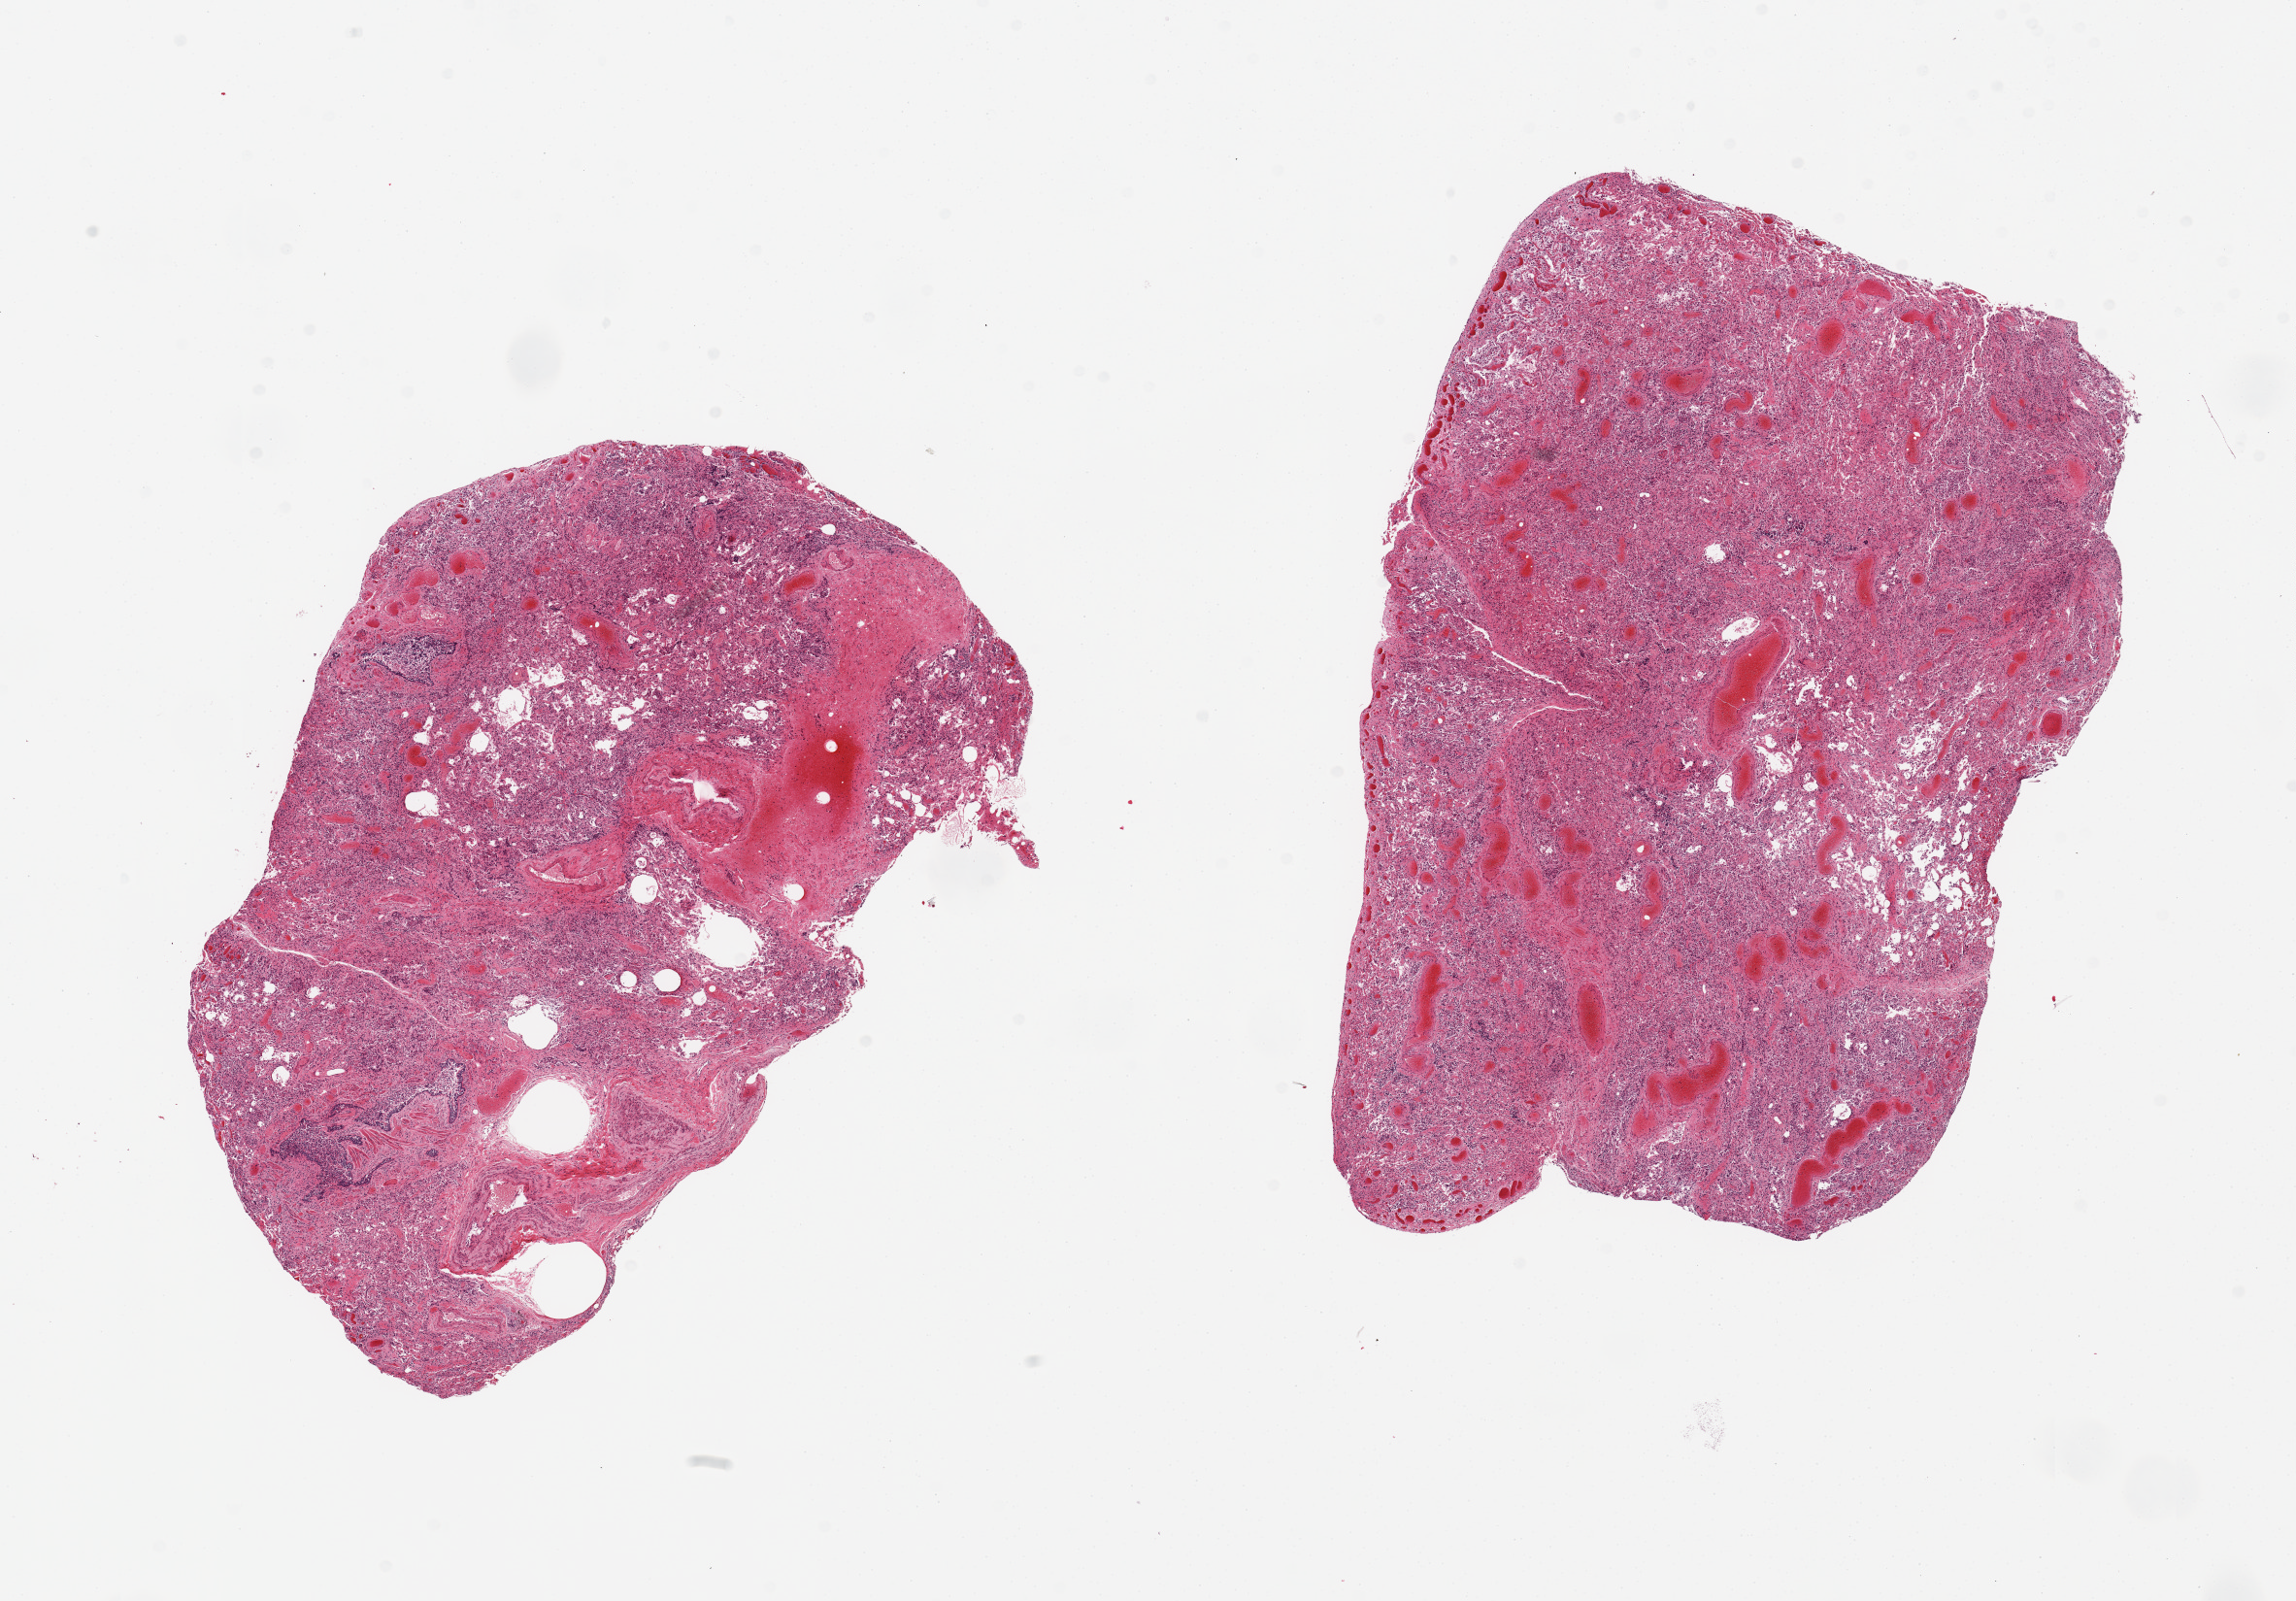
Whole-slide image, H&E stain, brightfield, shown as a low-resolution overview of the whole scanned area (about 18.7 x 13.0 mm, from a 20x scan); PAXgene-fixed, paraffin-embedded tissue; section of lung (target tissue); donor tissue sample. Male donor.
* reviewer comment on this tissue sample: 2 pieces; marked congestion; sloughing bronchial epithelium; collapsed alveolar spaces with many alveolar macrophages